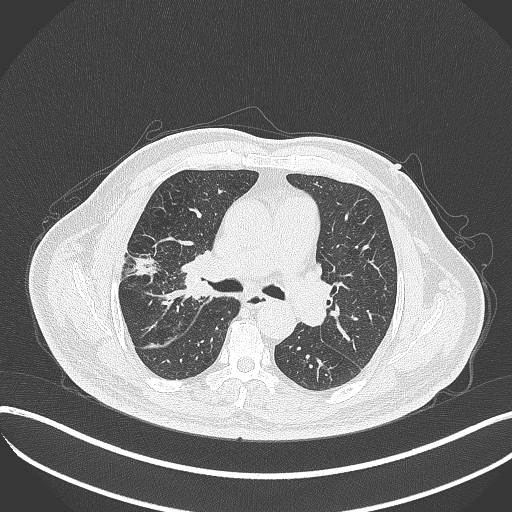
Chest CT, one axial slice; position 219 of 401 along the scan axis; reconstruction kernel B70f; lung window (W 1500 / L -600 HU); 512 × 512 image matrix. Patient: male, 72 years. Case-level facts recorded for this patient, not image findings: clinical TNM (as recorded): T1c N0 M0.
Structures marked on this image (bounding box drawn by a radiologist):
- lung tumour (recorded histology: squamous cell carcinoma): bounding box <173,247,205,306> (left, top, right, bottom; pixels)